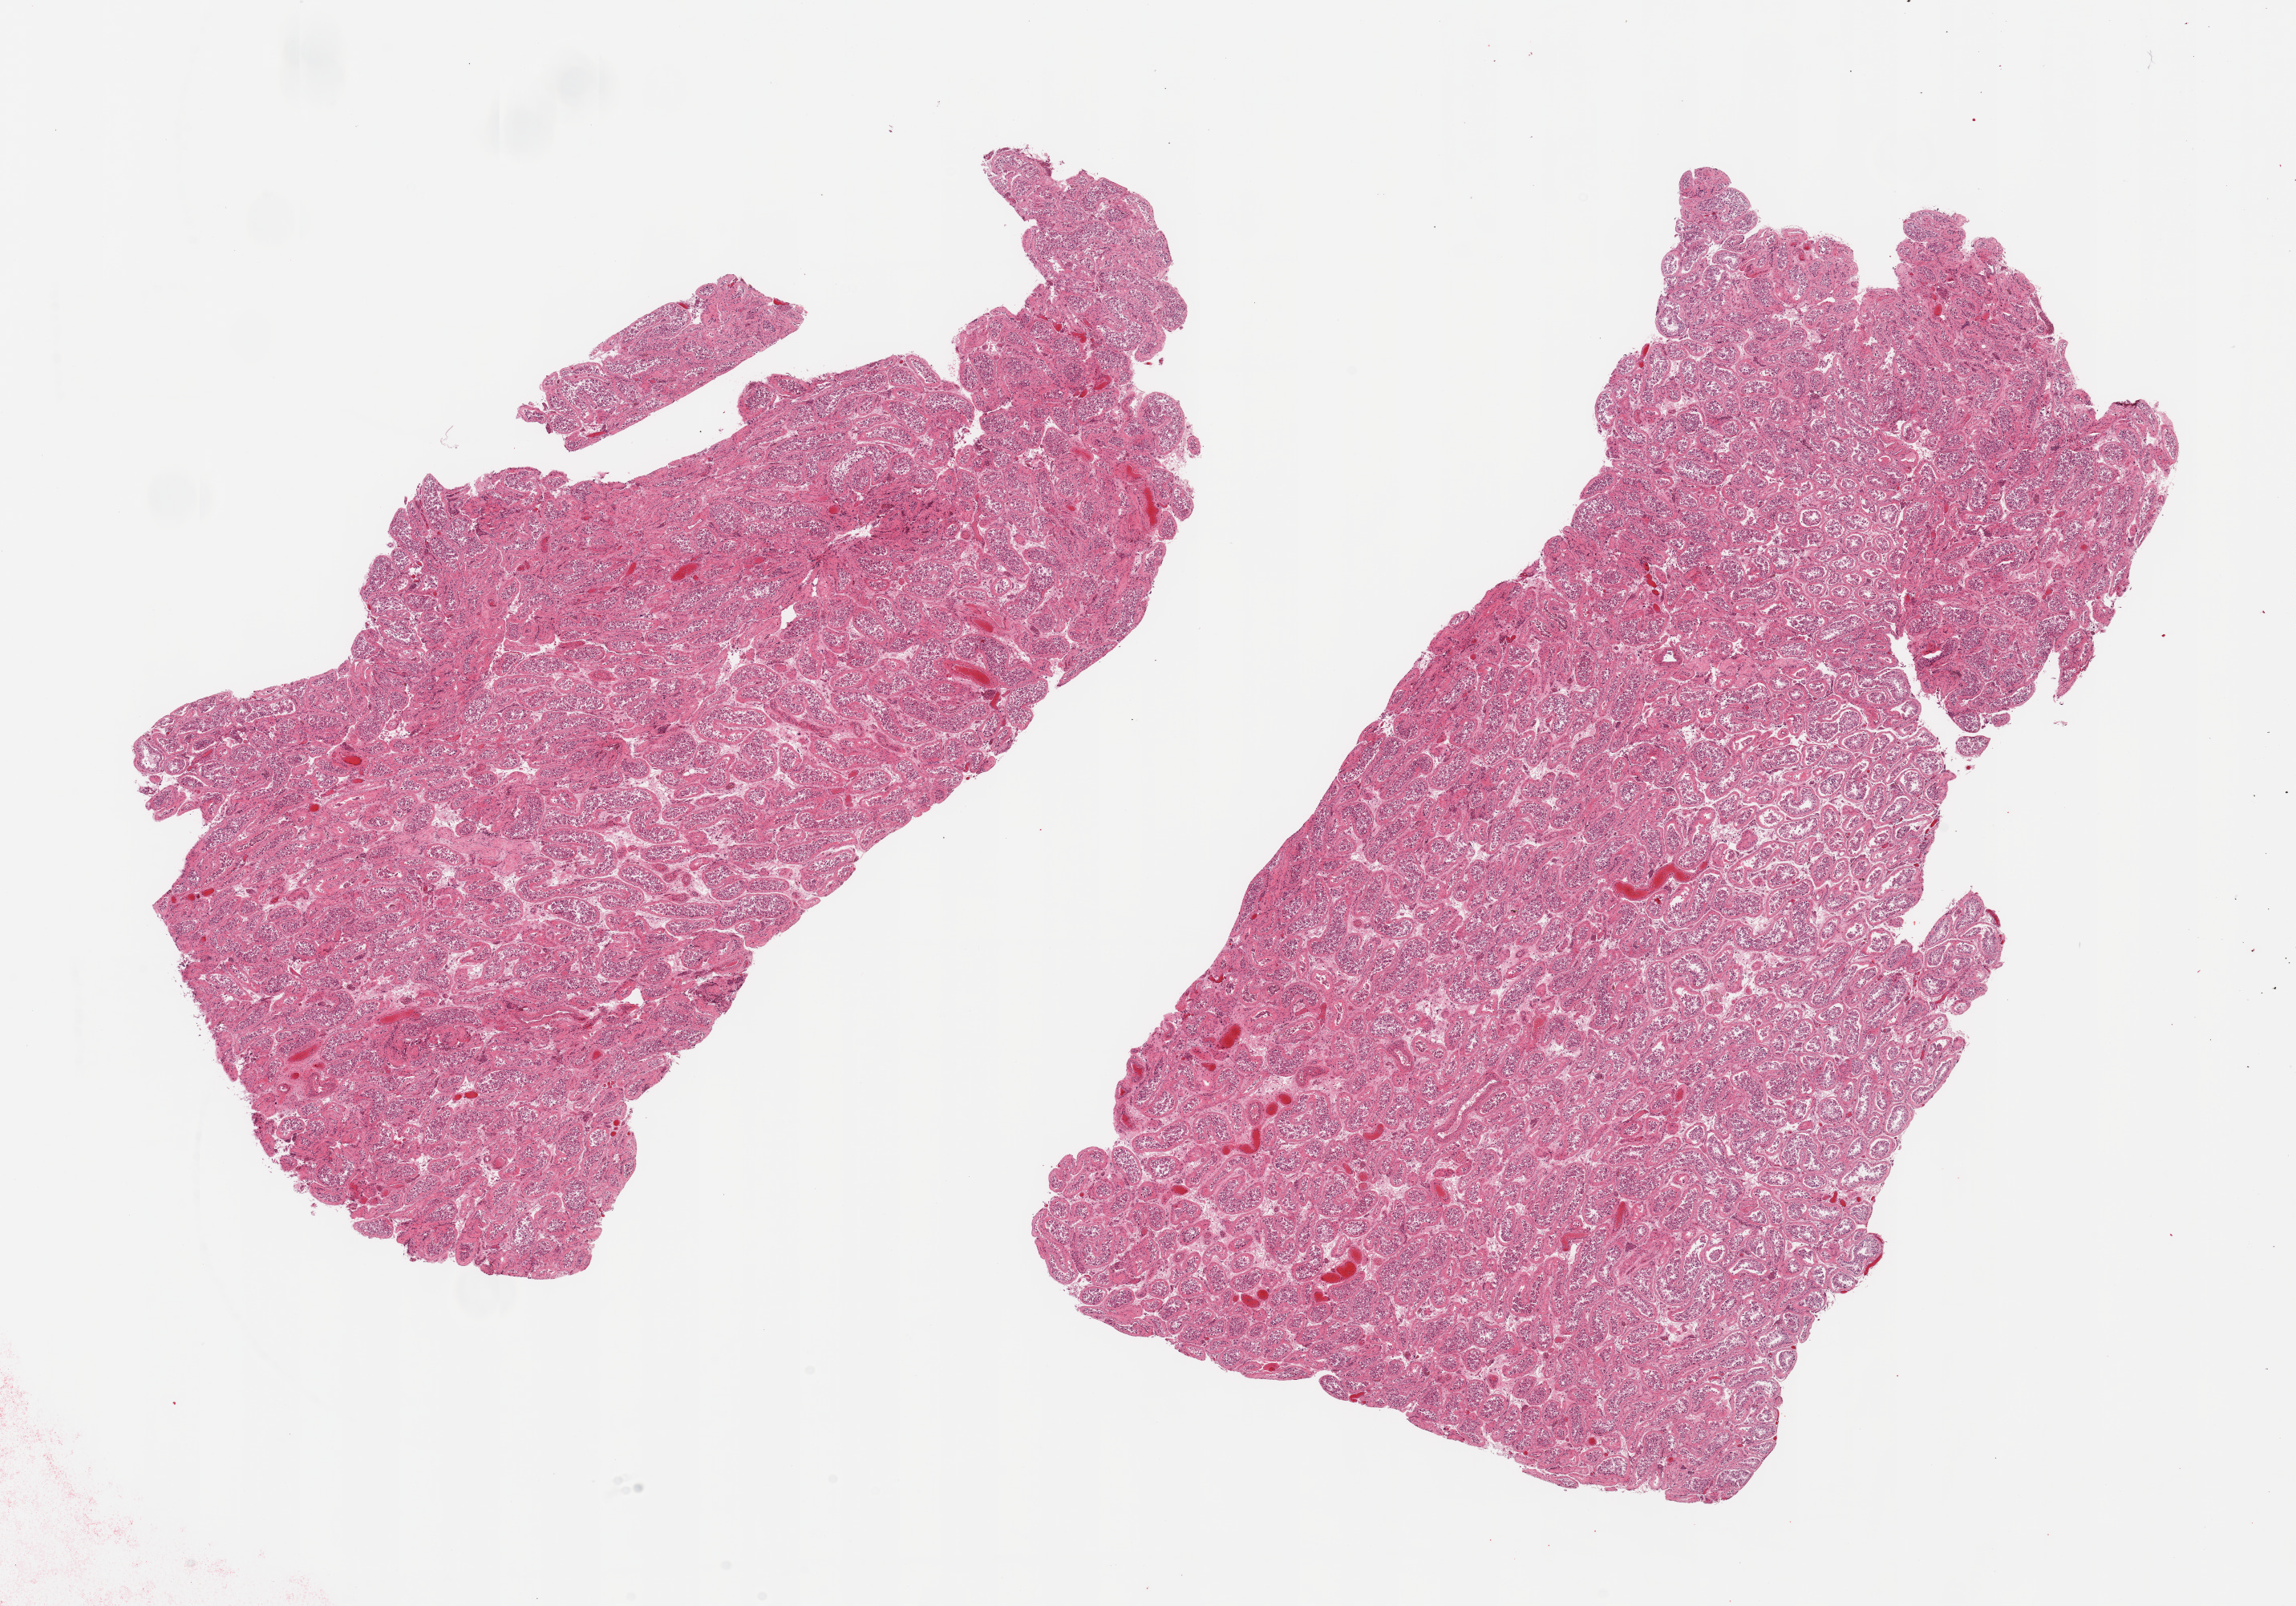
Digitized haematoxylin and eosin-stained section, low-resolution overview of the scanned area, about 22.6 x 15.8 mm. PAXgene-fixed, paraffin-embedded tissue. Sampled site (target tissue): testis. Tissue donor sample. Male donor.
Reviewer comment on this tissue sample: 2 pieces; reduced/absent spermatogenesis.